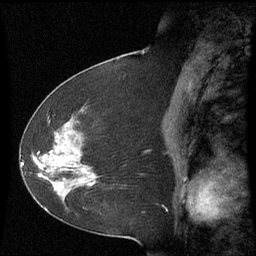
Breast MRI (dynamic contrast-enhanced), one sagittal slice; position 30 of 60 along the scan axis; dynamic contrast-enhanced series, image 2 of 3 at this slice position (ordered by acquisition); 1.5 T; TE 4.2 ms, TR 8.9 ms; 2.3 mm slice thickness; 256 × 256 image matrix, field of view 210 × 210 mm. Female patient, age 51 years. From the clinical record (not read from this slice): setting: breast cancer imaged before/during neoadjuvant chemotherapy; receptor status: HR-positive, HER2-negative.
Structures marked on this image (semi-automatic segmentation, software-assisted and operator-edited):
- analysis volume of interest (the breast-tissue region the enhancement analysis was run in; not a lesion): bounding box [x1, y1, x2, y2] px = [50, 119, 100, 187]
- tumour enhancement mask (voxels above the 70 % enhancement threshold inside the analysis volume of interest): [75, 165, 93, 185]